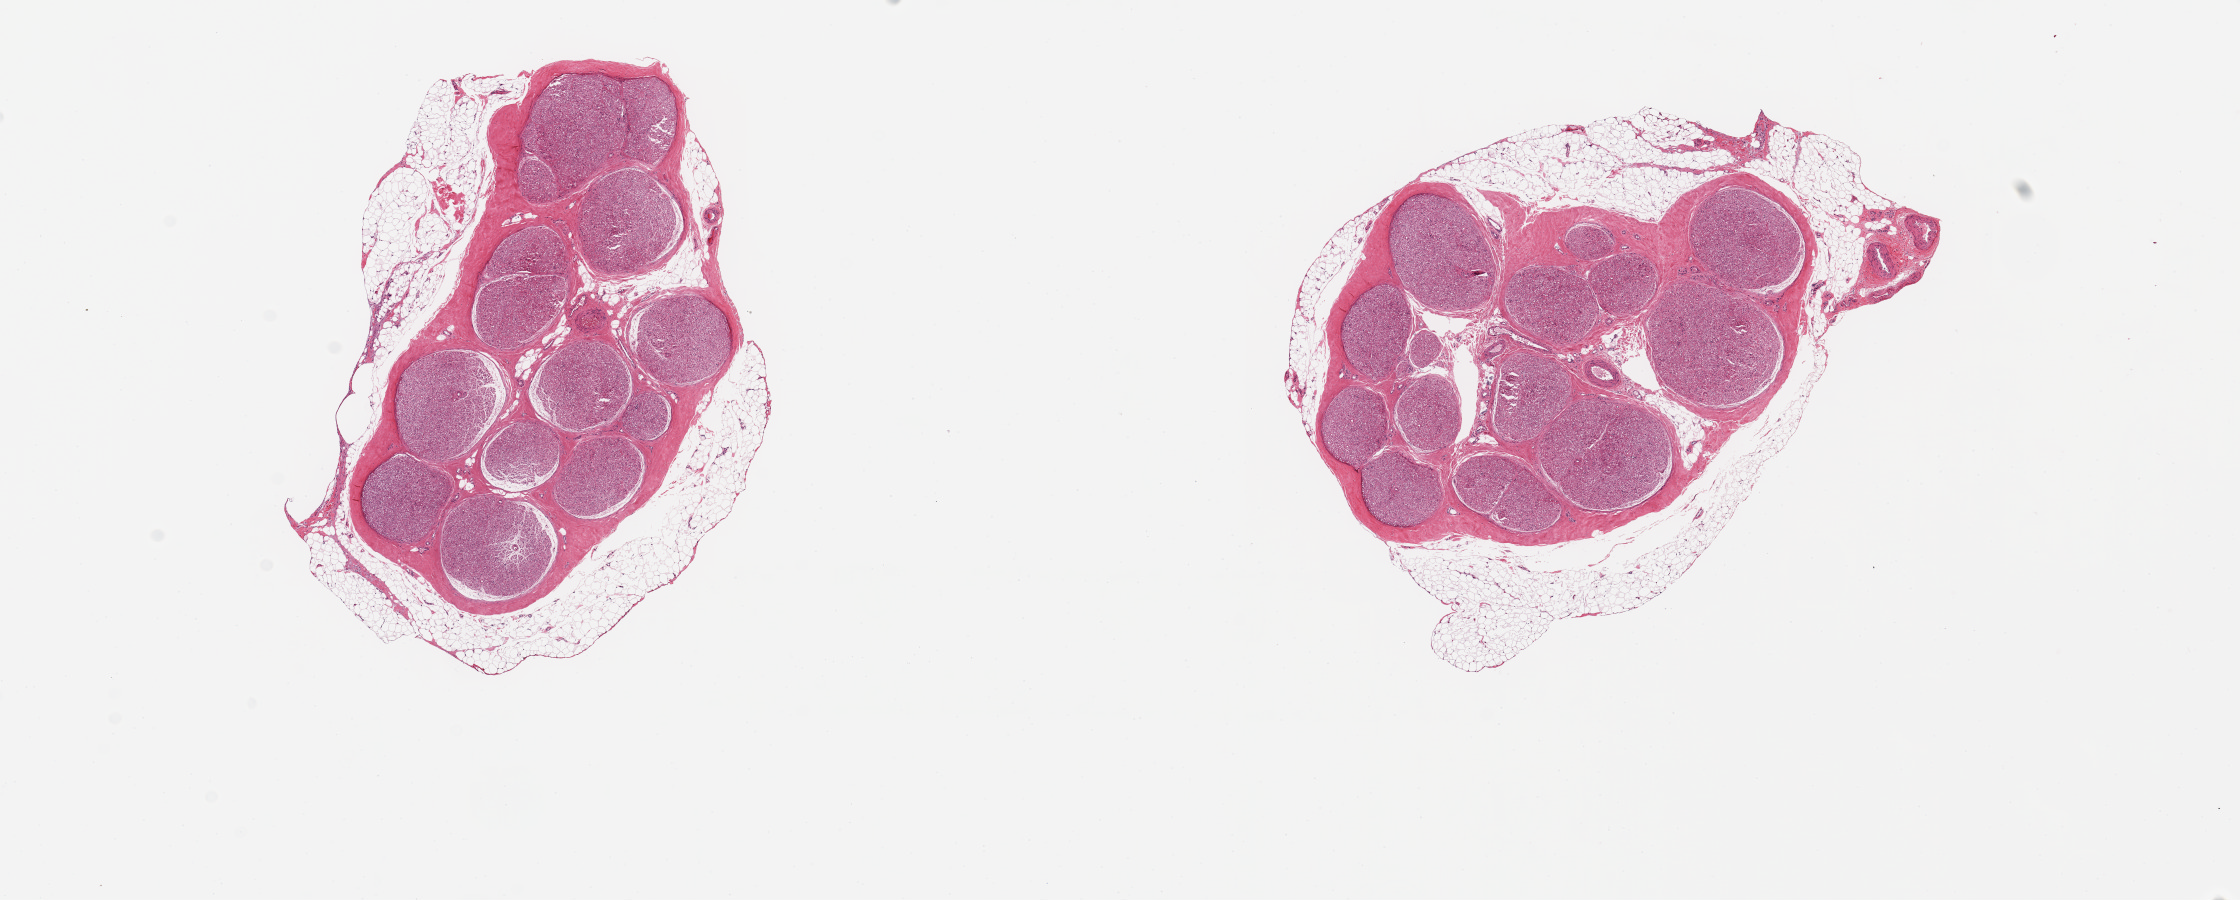
Whole-slide image, haematoxylin and eosin stain, a low-resolution overview of the entire scanned area, about 17.7 x 7.1 mm (acquisition: 20x scan). PAXgene-fixed, paraffin-embedded tissue. Target tissue: tibial nerve. Donor tissue sample. Donor sex: male.
Pathologist's review note for this sample: 2 pieces,~4x2mm;4.5x3.5mm; ~30% fat on outside of each piece.